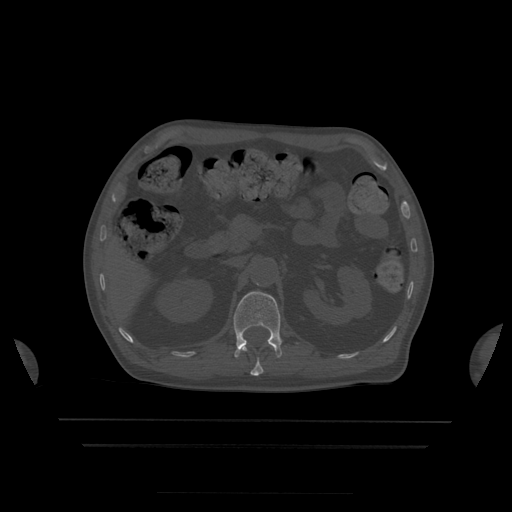
CT including the spine, one axial slice; position 179 of 522 along the scan axis; bone window (W 1800 / L 400 HU); 1.25 mm slice thickness; 512 × 512 image matrix, field of view 436 × 436 mm. Patient age 68 years. Case-level facts recorded for this patient, not image findings: primary cancer: urothelial.
Outlined on this slice (semi-automatic segmentation, software-assisted and operator-edited):
- L1 vertebra: bounding box <234,292,283,358> (left, top, right, bottom; pixels)
- T12 vertebra: <243,346,263,376>